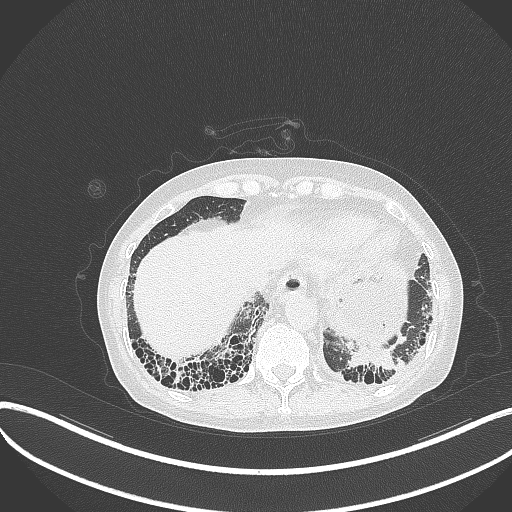
Chest CT, one axial slice. Position 57 of 373 along the scan axis. Reconstruction kernel B70f. Lung window (W 1500 / L -600 HU). 512 × 512 image matrix, field of view 400 × 400 mm. Female patient, age 56 years. From the clinical record (not read from this slice): clinical TNM (as recorded): T1 N0 M0.
Outlined on this slice (bounding box drawn by a radiologist):
- lung tumour (recorded histology: adenocarcinoma): box from (x=345, y=345) to (x=410, y=373) px